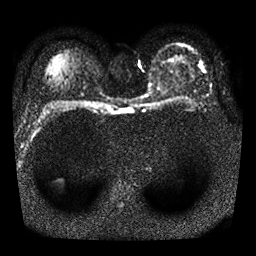
Breast MRI, one axial slice. Position 19 of 25 along the scan axis. Diffusion-weighted series; image 2 of 4 stored at this slice position (different b-values; order by instance number). 1.5 T. 4 mm slice thickness. 256 × 256 image matrix. Female patient.
Annotated regions visible in this slice (manually delineated by an expert):
- tumour on diffusion-weighted imaging: box from (x=157, y=83) to (x=160, y=89) px